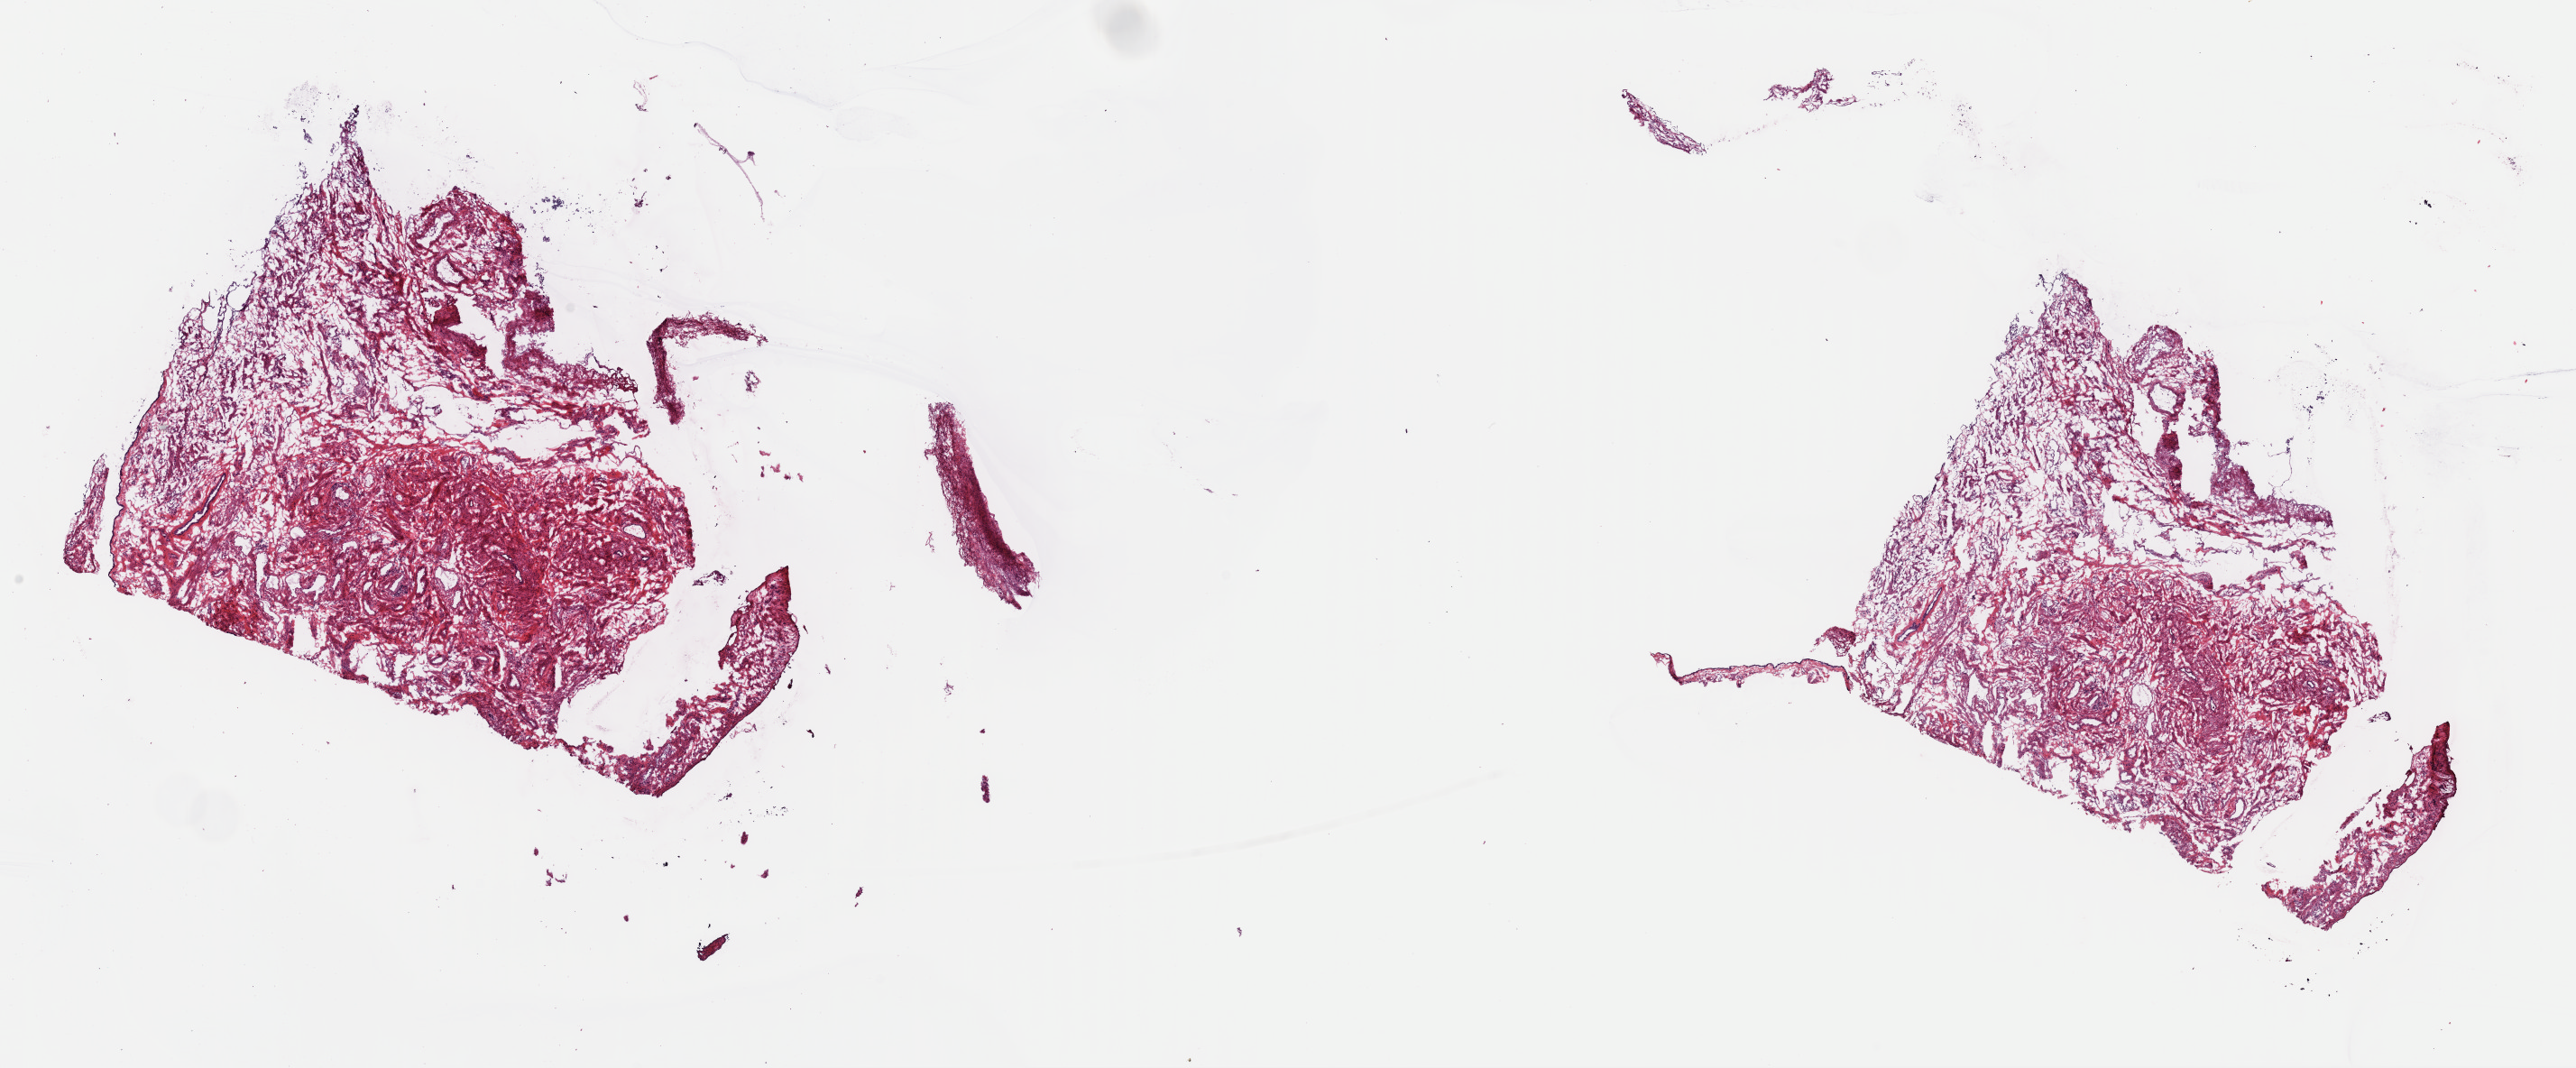
Digitized Hematoxylin and eosin (H&E) stained tissue section (whole slide) — shown as a low-resolution overview of the whole scanned area (about 22.6 x 9.4 mm), frozen section from the top of the tissue portion, primary tumour sample from the uterus. Female patient; age at initial diagnosis 69 years. Histologic grade: G3 (poorly differentiated). Slide review estimates, as recorded: tumour cells 96%, tumour nuclei 96%, normal cells 0%, stromal cells 2%, necrosis 2%. Infiltration values recorded for this section: lymphocyte infiltration 1%, monocyte infiltration 0%, neutrophil infiltration 0%.
Histologic diagnosis: Endometrioid adenocarcinoma, NOS (endometrium). FIGO stage: IIIA. Lymph nodes positive (case pathology): 0 of 5 examined.